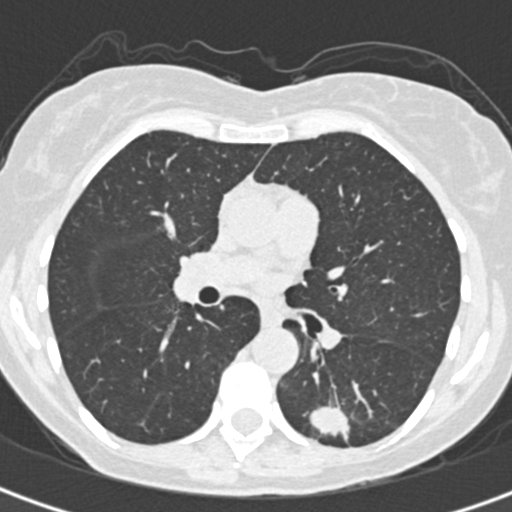
Low-dose screening chest CT, one axial slice; position 191 of 328 along the scan axis; reconstruction kernel B30f; lung window (W 1500 / L -600 HU); 1 mm slice thickness; 512 × 512 image matrix.
Annotated regions visible in this slice (expert manual segmentation):
- lesion 1 (tumor, lower lobe of left lung): box from (x=310, y=405) to (x=350, y=439) px